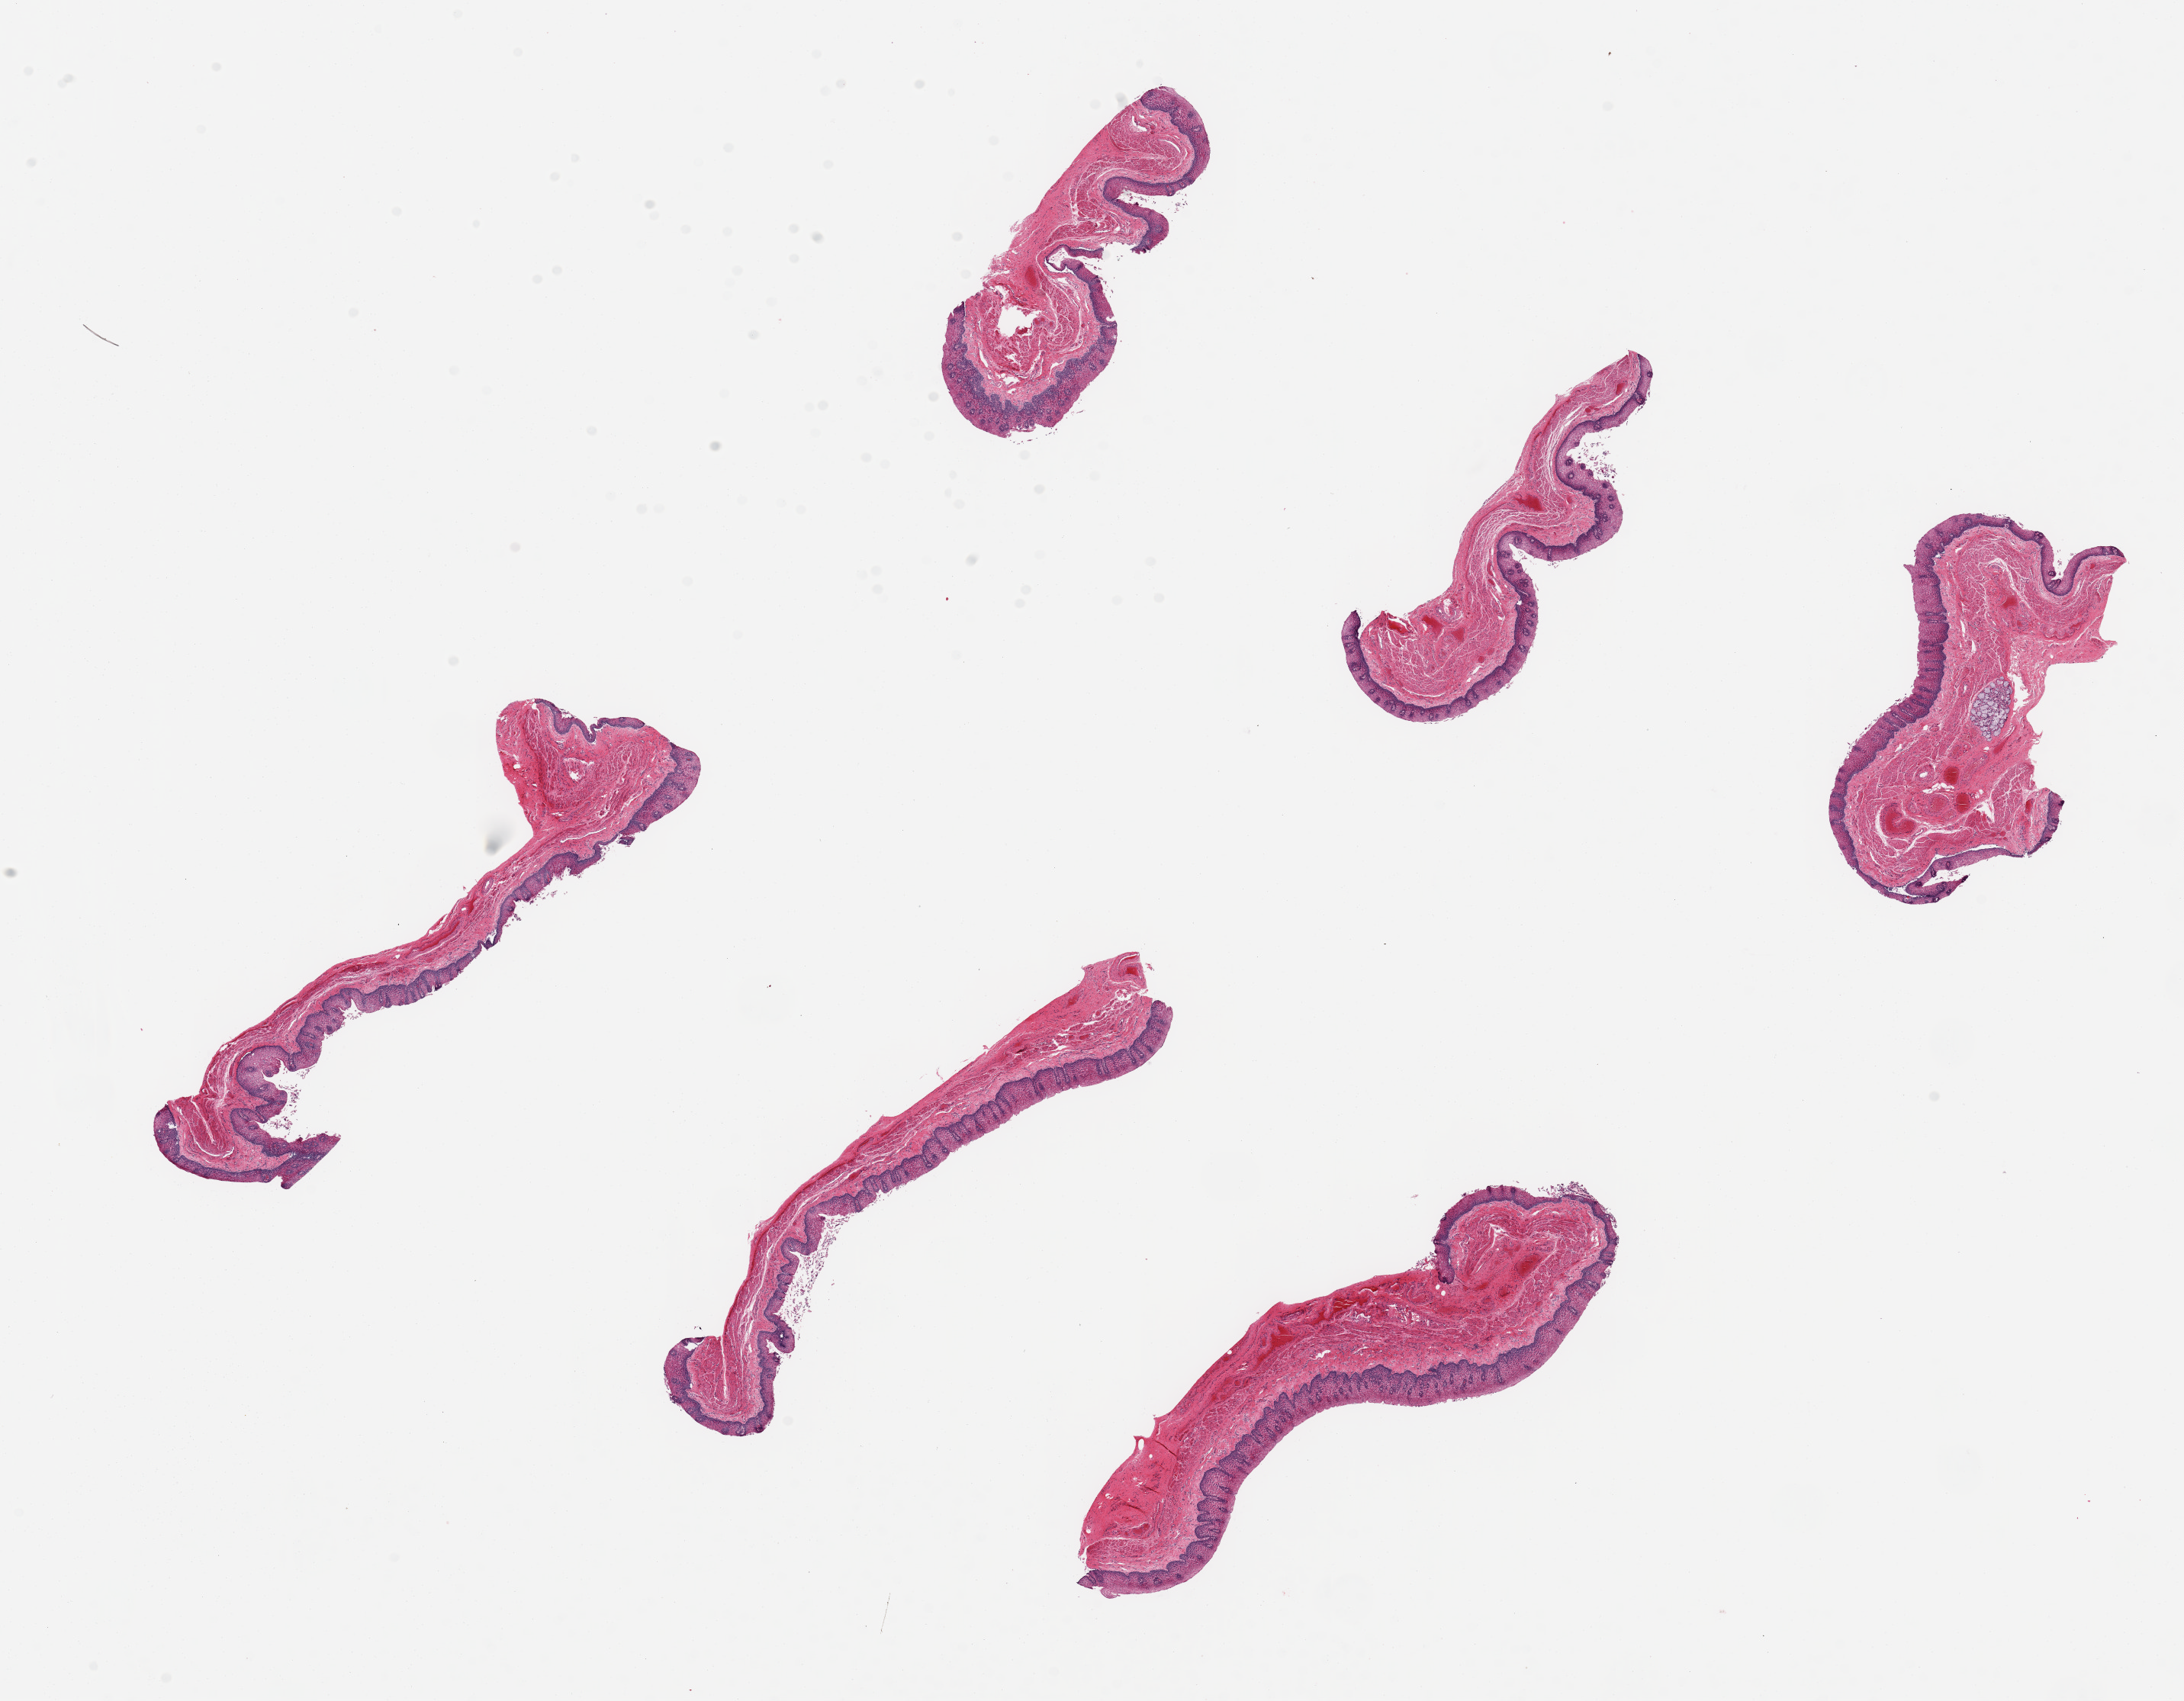
Whole-slide image, hematoxylin and eosin (H&E) stain, brightfield, shown as a low-resolution overview of the whole scanned area (about 22.6 x 17.6 mm, slide scanned at 20x). PAXgene-fixed paraffin-embedded (PFPE) section. Sampled site (target tissue): esophageal mucous membrane. Tissue donor sample. Female donor.
- review note (as recorded): 6 pieces up to 6x2 mm